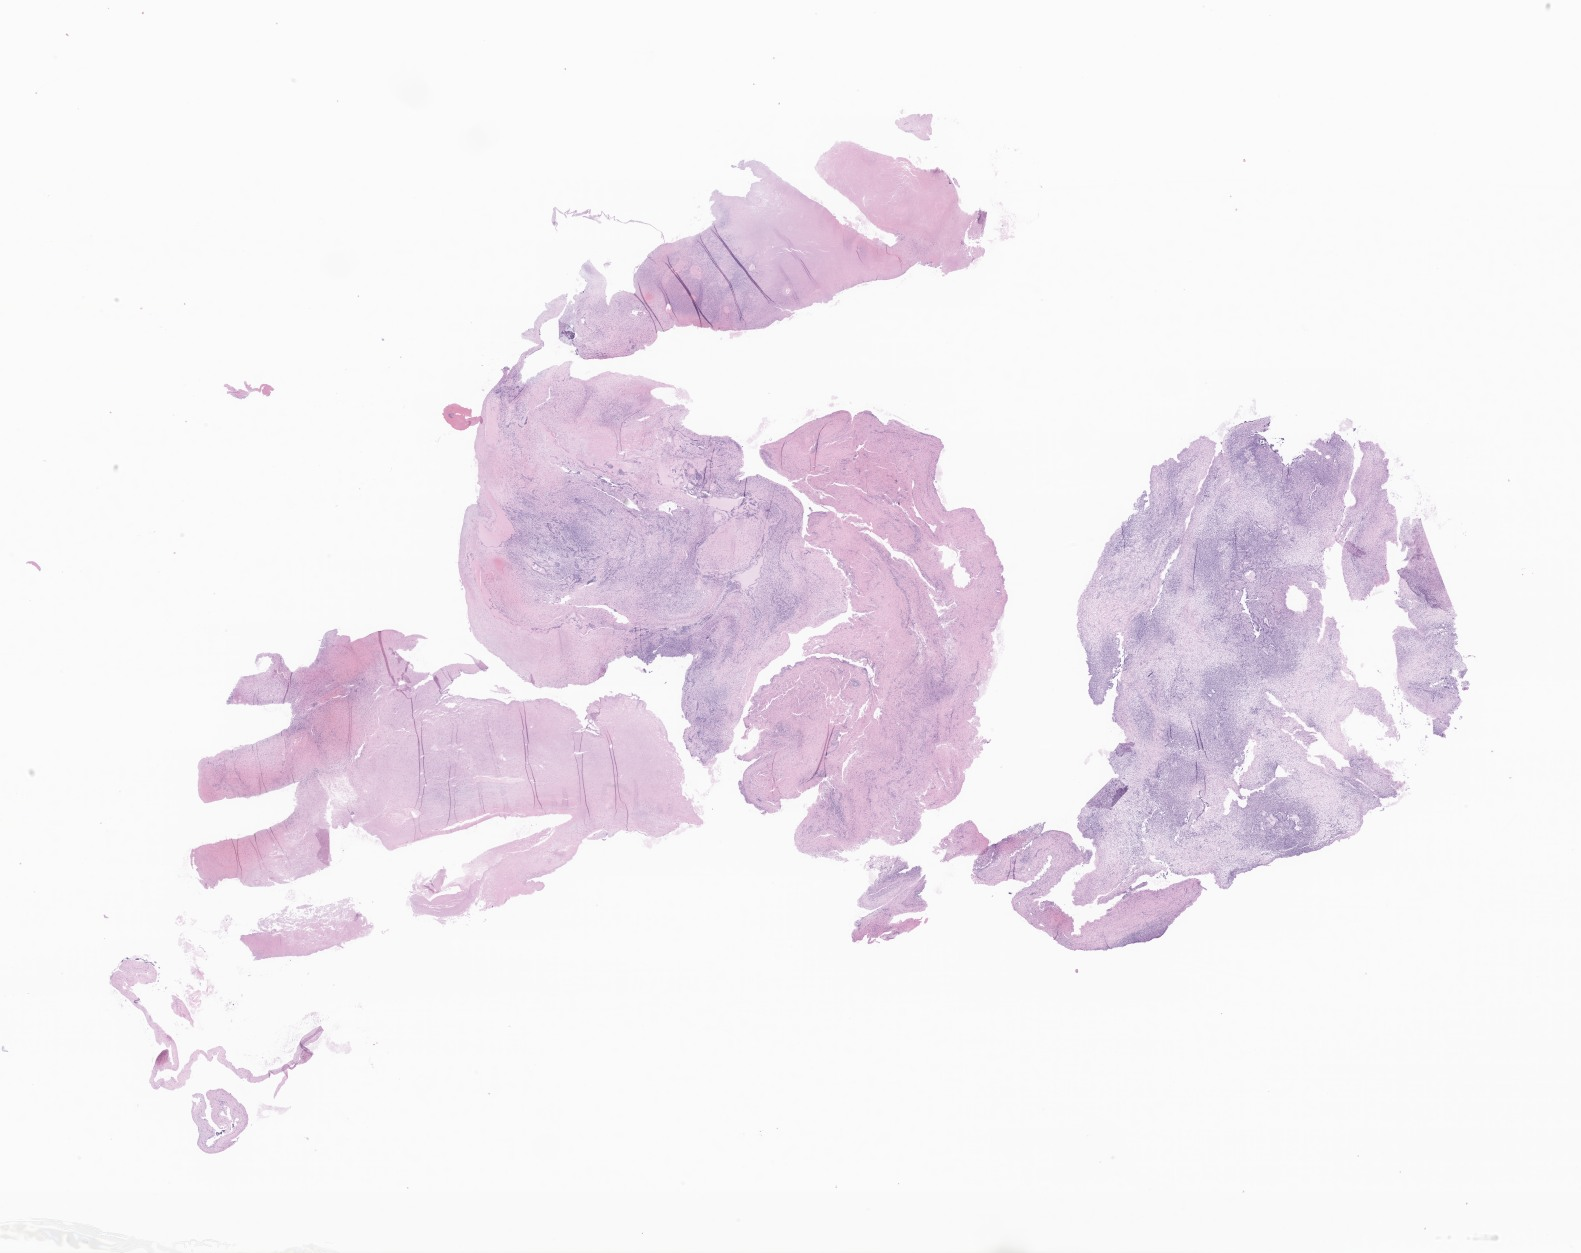
Digitized hematoxylin and eosin (H&E)-stained section of tumor tissue from the ovary — a low-resolution overview of the entire scanned area, about 26.7 x 21.1 mm, formalin-fixed, paraffin-embedded (FFPE) tissue. Patient: female, age 187 months (15 years 7 months).
Diagnosis (ICD-O-3 morphology term): Sertoli-Leydig cell tumor, poorly differentiated.